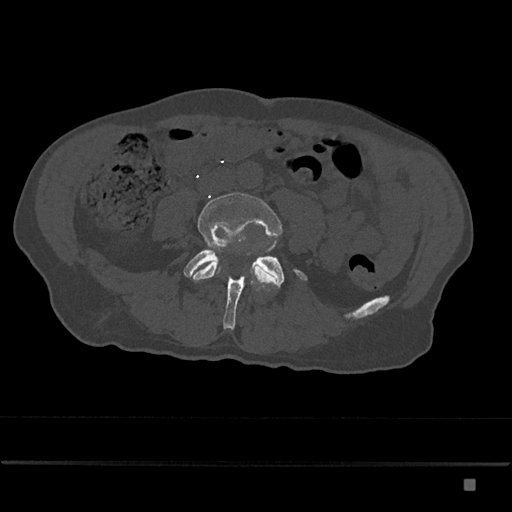
CT including the spine, one axial slice; reconstruction kernel Br40s/3; bone window (W 1800 / L 400 HU); 0.5 mm slice thickness; 512 × 512 image matrix. Male patient, age 72 years. Case-level facts recorded for this patient, not image findings: primary cancer: prostate.
Outlined on this slice (semi-automatically segmented with operator editing):
- L4 vertebra: bounding box (x1, y1, x2, y2) in pixels: (189, 192, 283, 285)
- L5 vertebra: (183, 245, 308, 330)